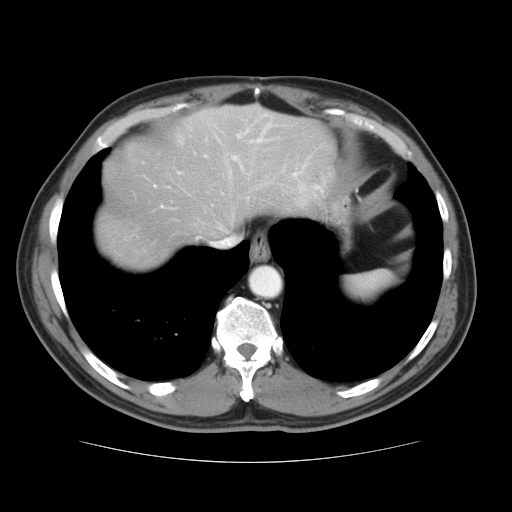
Contrast-enhanced abdominal CT, one axial slice. Position 31 of 37 along the scan axis. 120 kVp. Intravenous contrast given. Soft-tissue window (W 400 / L 40 HU). 512 × 512 image matrix, field of view 374 × 374 mm. Male patient, age 66 years. Case-level facts recorded for this patient, not image findings: diagnosis: colorectal cancer liver metastases, imaged before liver resection; multiple liver metastases: yes; largest metastasis: 1.6 cm; disease in both lobes: yes.
Structures marked on this image (outlined manually by an expert reader):
- hepatic veins: bounding box <211,168,243,244> (left, top, right, bottom; pixels)
- liver: <95,106,336,271>
- planned liver remnant (the part of the liver to remain after resection): <97,109,336,271>
- portal vein (with intrahepatic branches): <154,124,271,207>